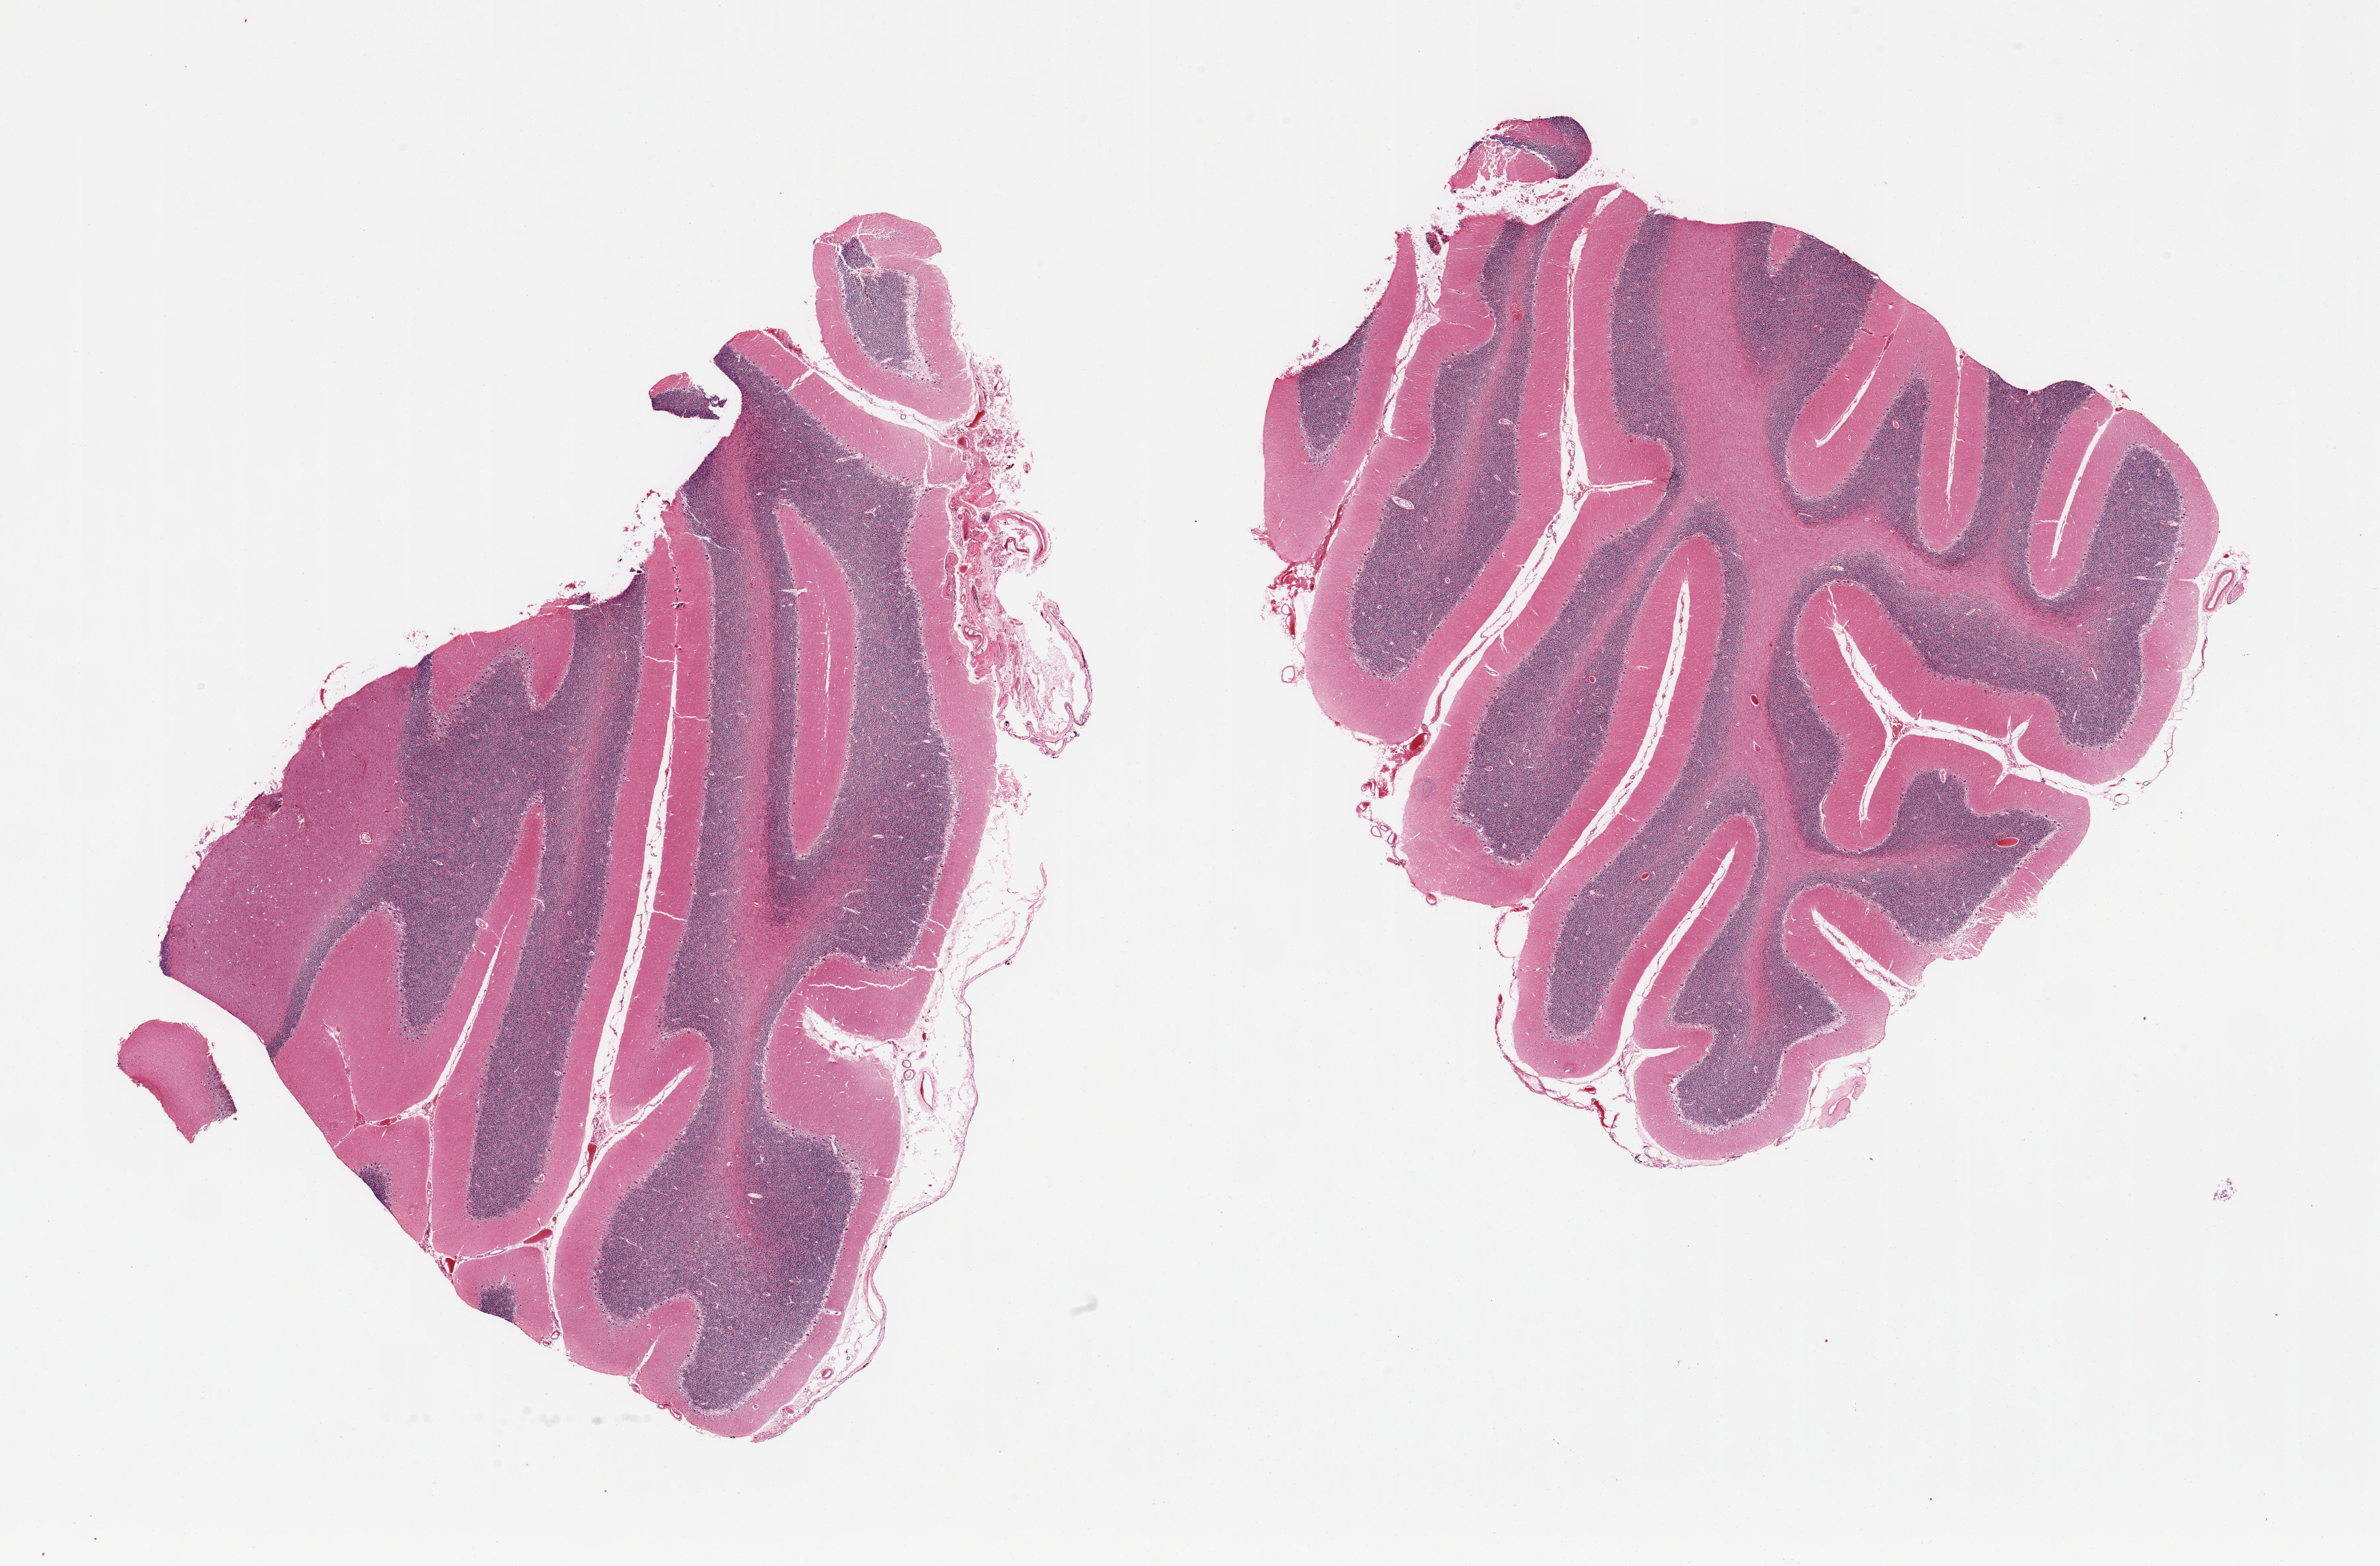
Digitized H&E-stained section, whole scanned area (about 28.5 x 18.8 mm, from a 20x scan) shown as a low-resolution overview; PAXgene-fixed paraffin-embedded (PFPE) section; target tissue: cerebellum; donor tissue sample. Male donor.
* review note (as recorded): 2 pieces; mild to moderate autolysis, residual attached mininges, Purkinje cells well visualized